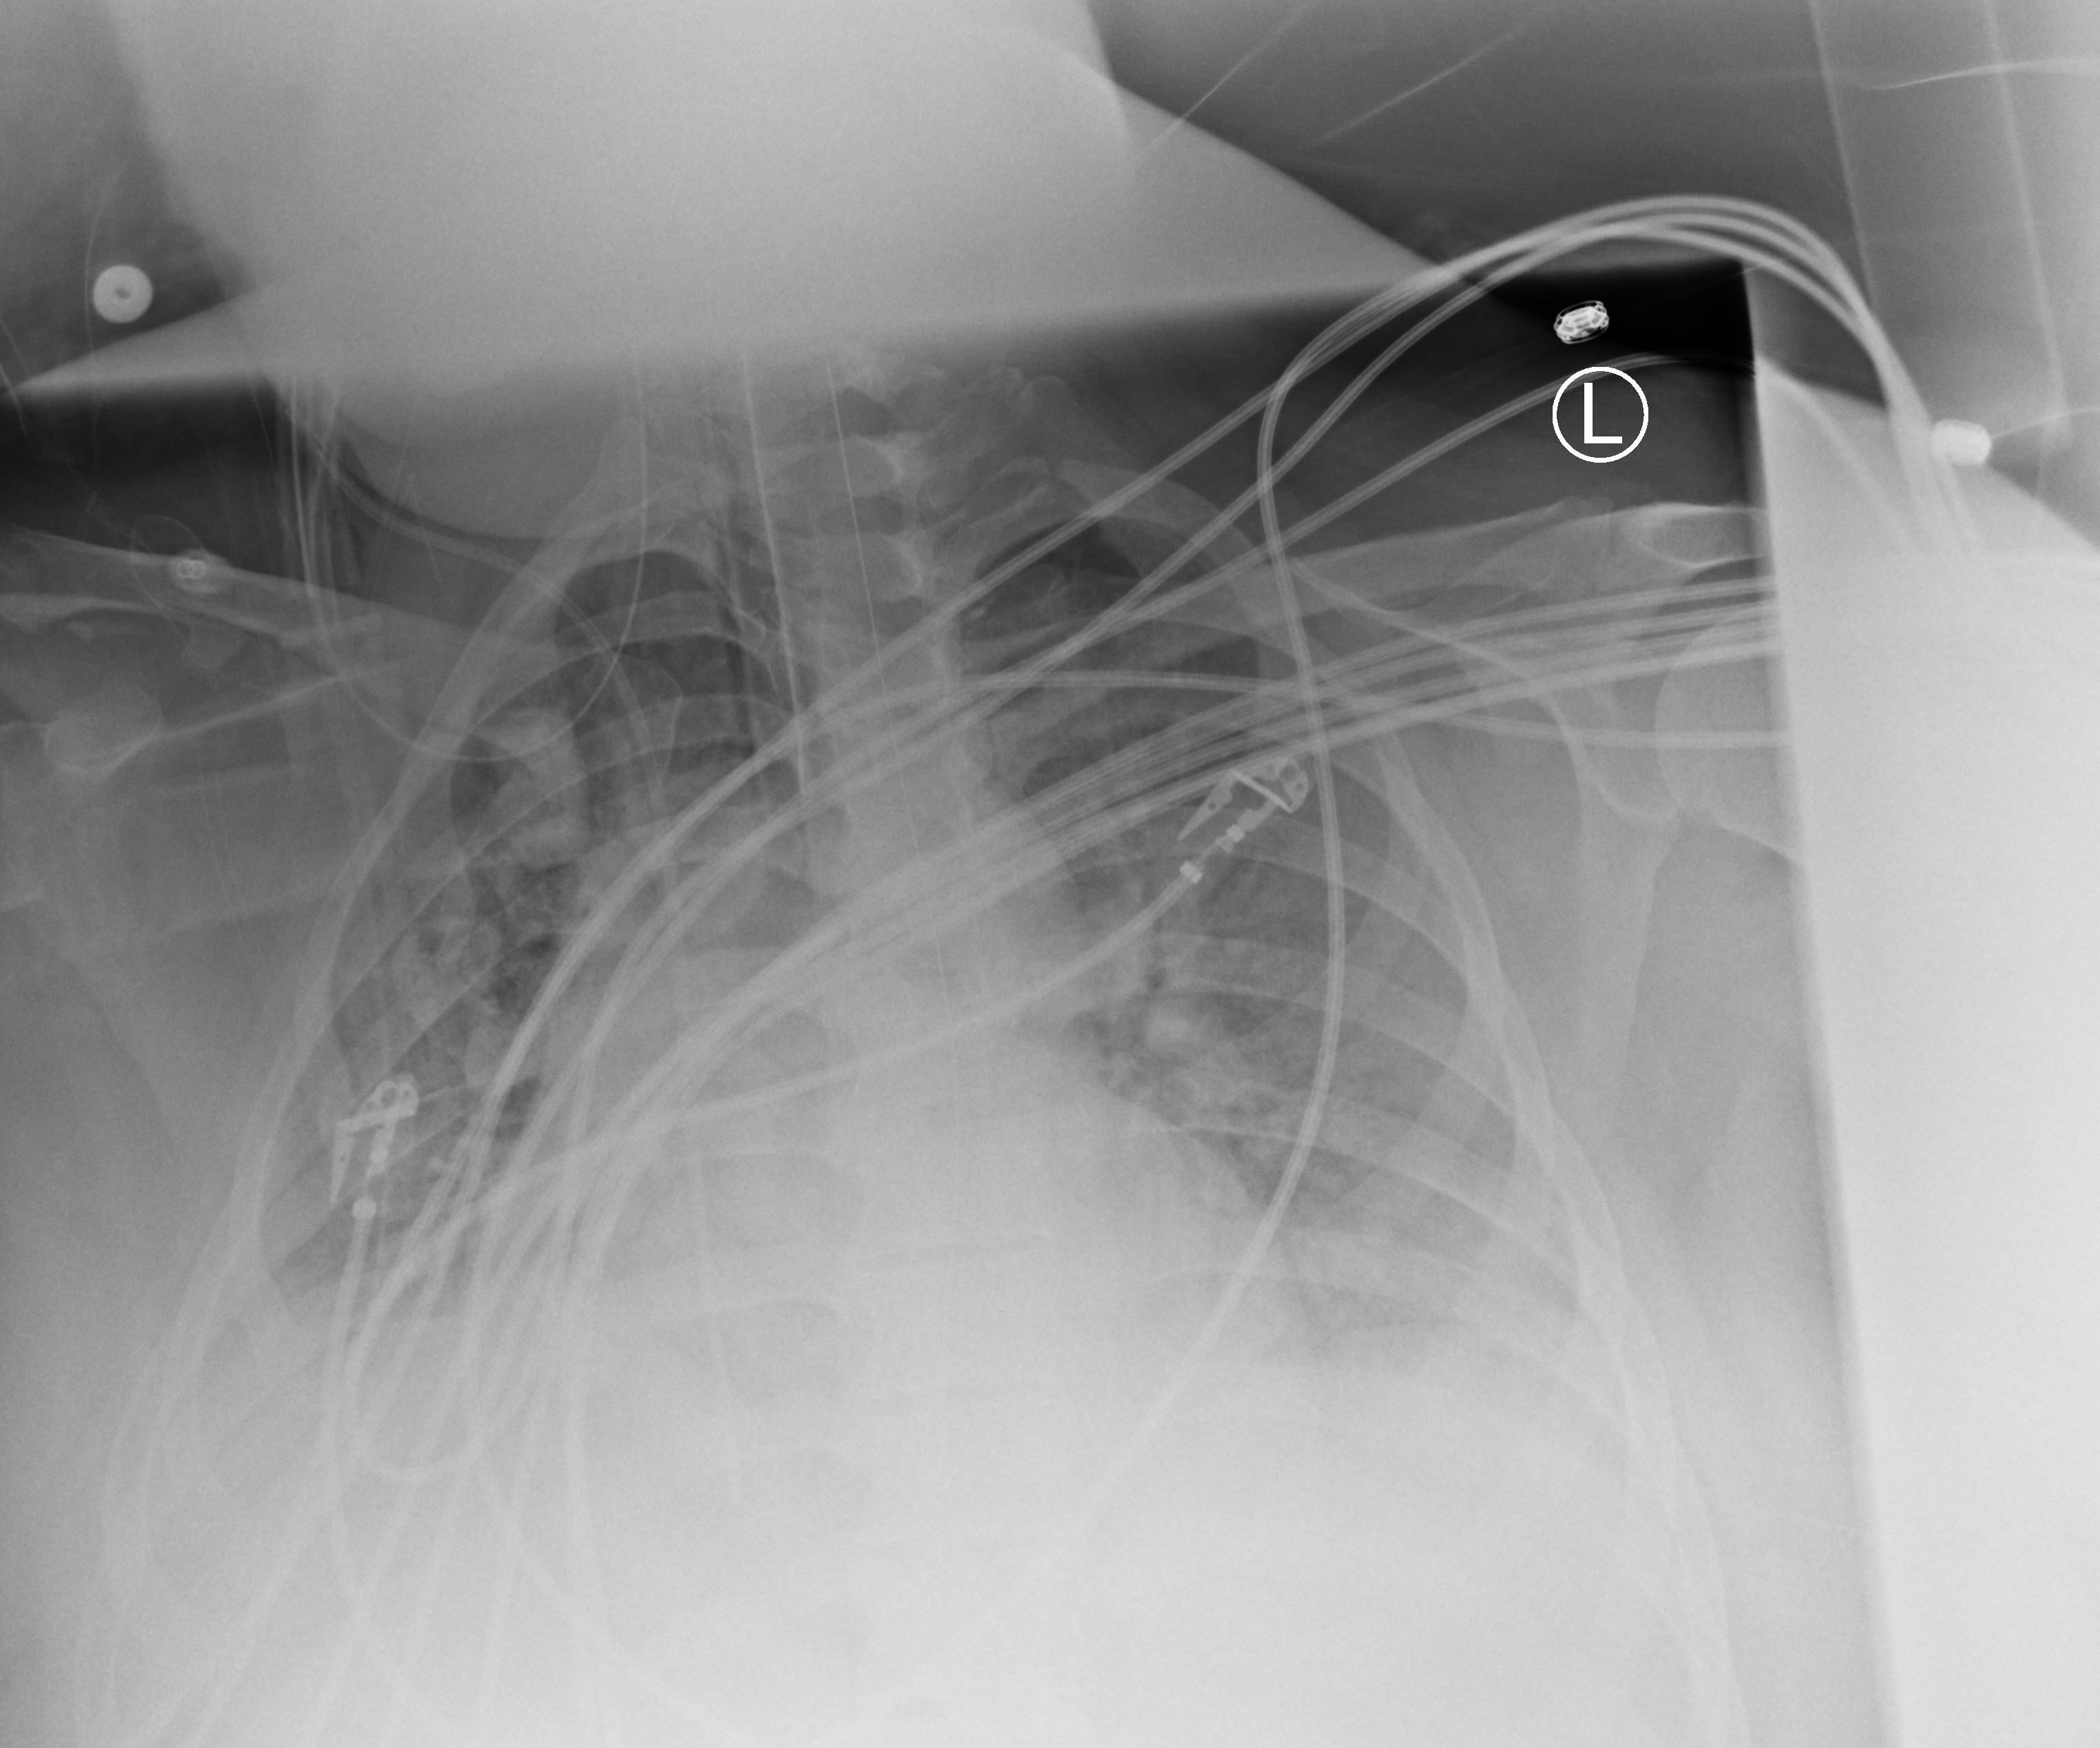
Portable chest radiograph; anteroposterior (AP) projection. Patient hospitalised with COVID-19; female, aged 18–59 years.
Admission-level facts for this patient (not findings on this image; timing relative to this image not recorded):
- length of hospital stay: 25 days